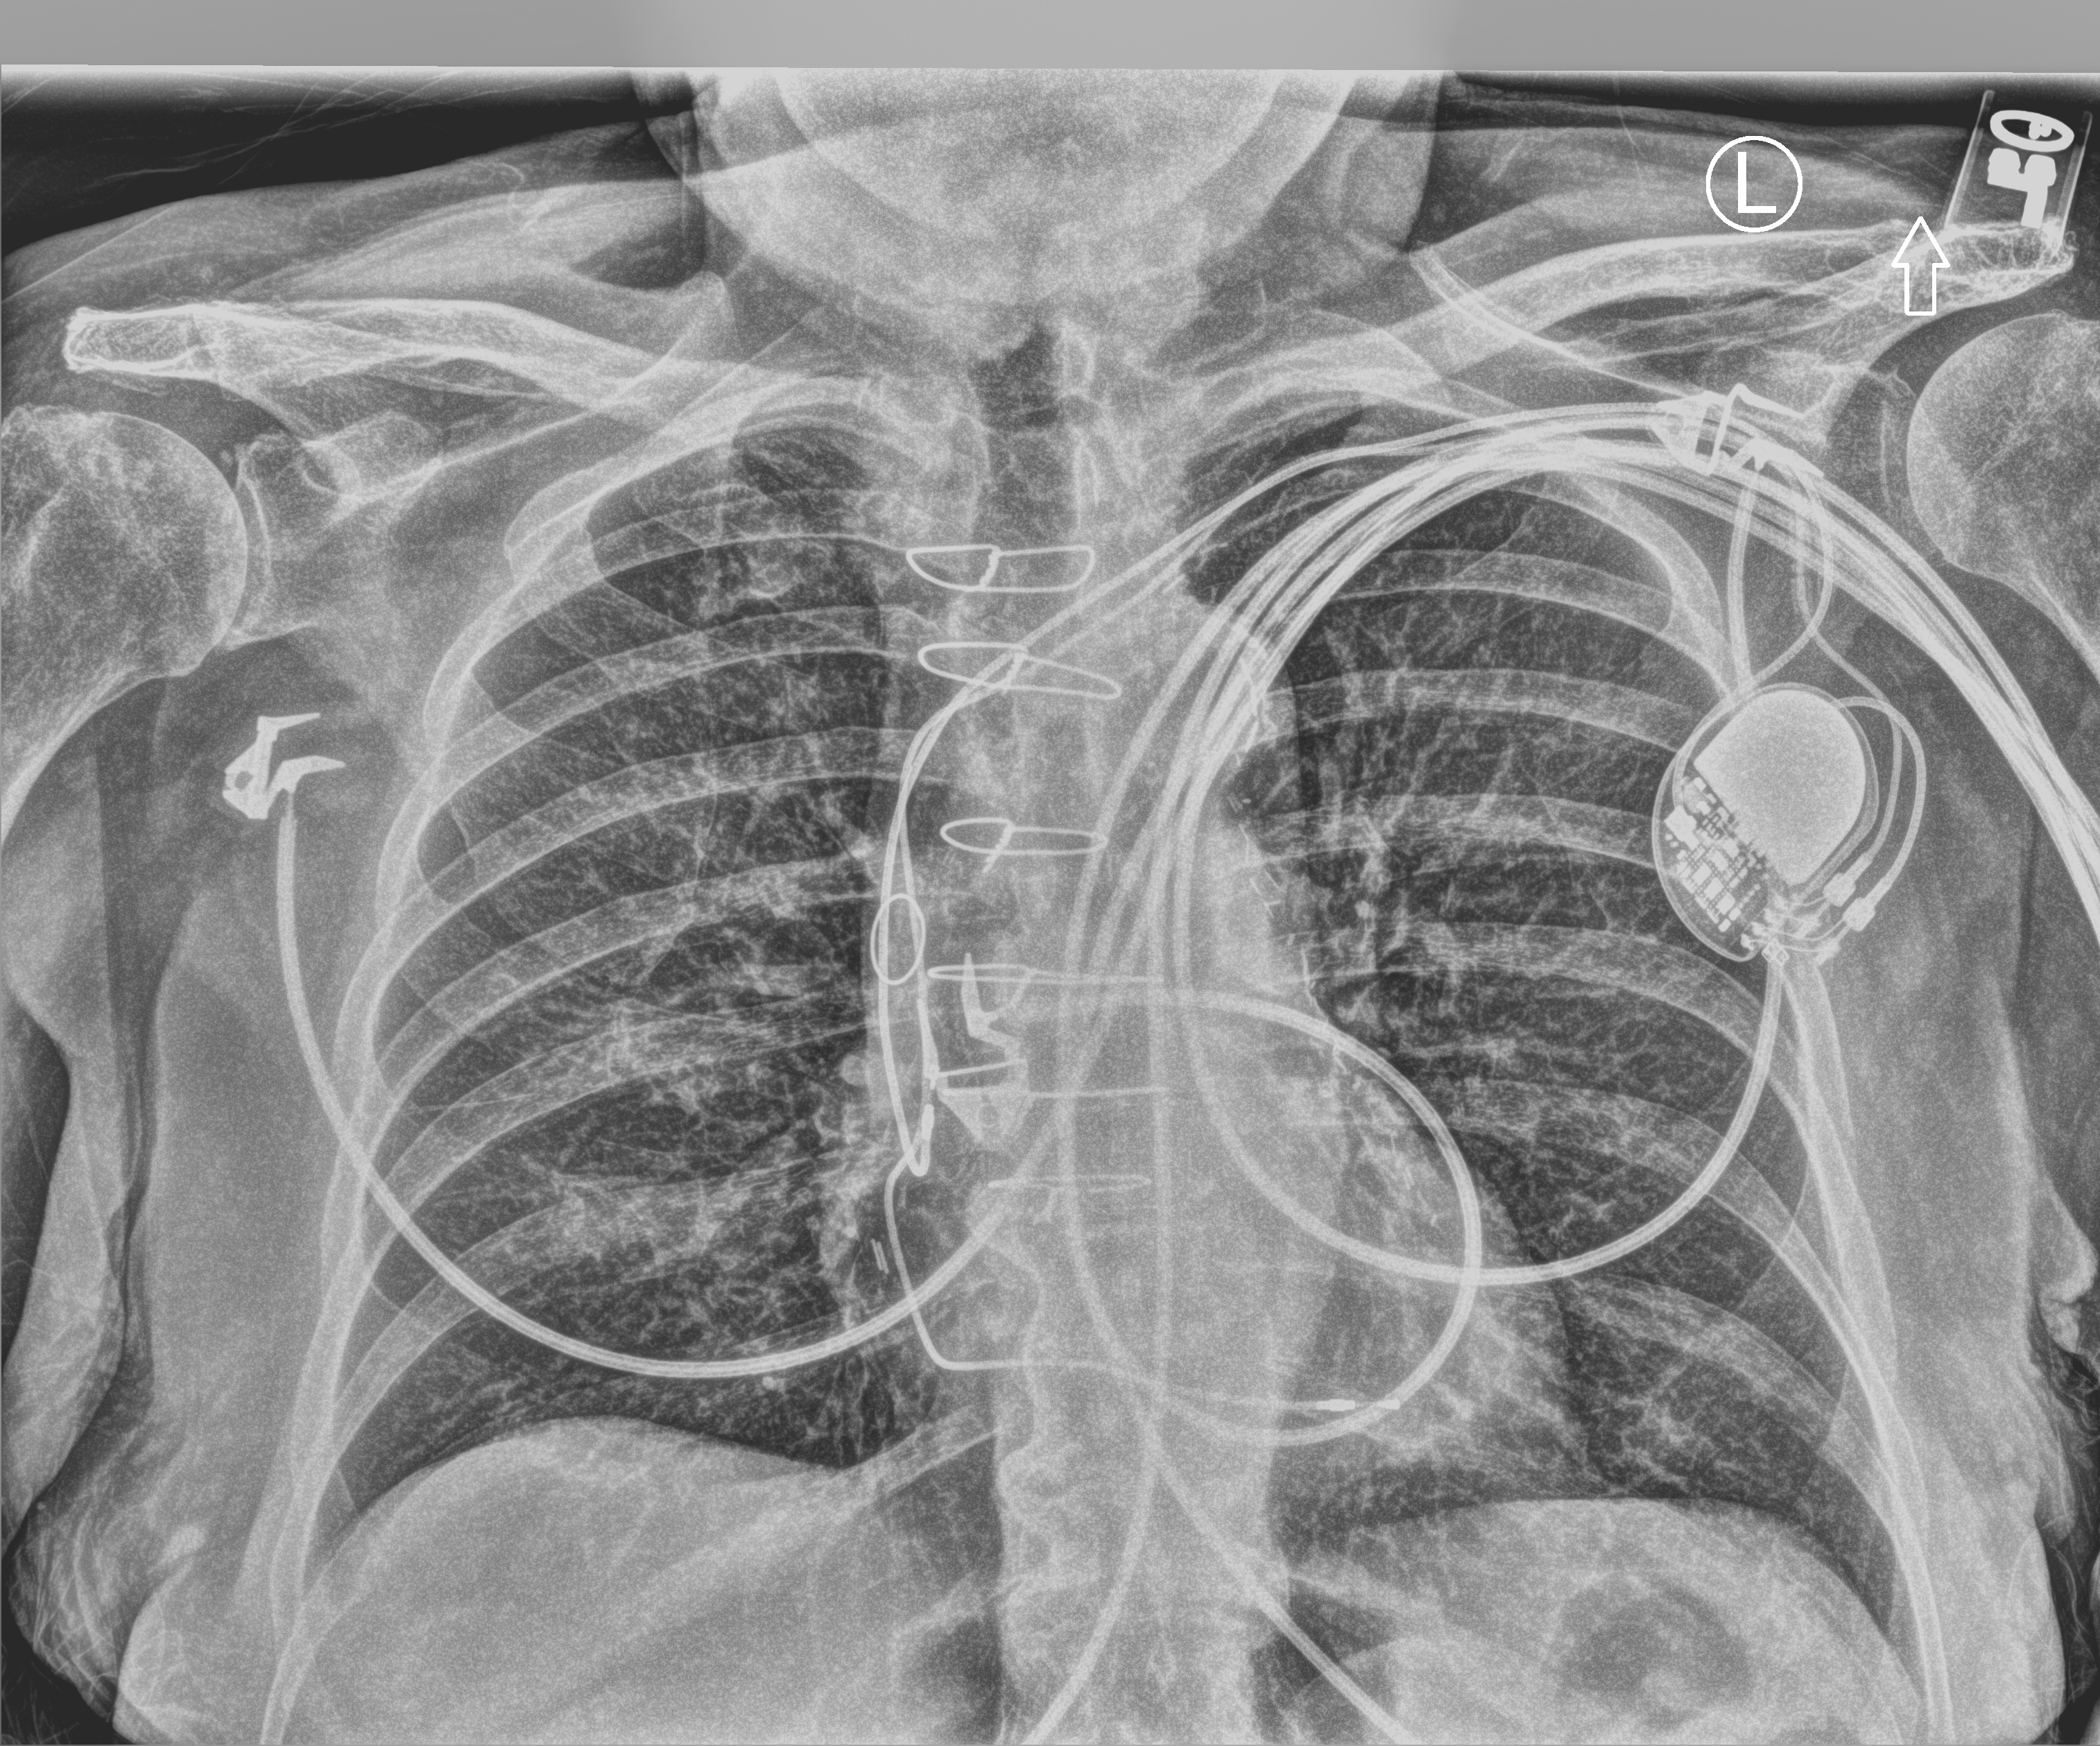
Chest X-ray (portable); anteroposterior (AP) projection. Female patient hospitalised with COVID-19, age 75–90 years.
From the hospital-stay record, not from the radiograph (when in the stay this image was taken is not recorded): mechanically ventilated during this hospital stay: no; length of hospital stay: 5 days; admitted to intensive care during this hospital stay: no.